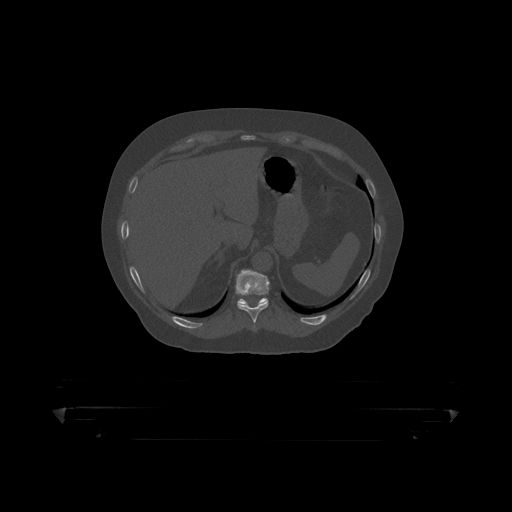
CT including the spine, one axial slice; position 210 of 390 along the scan axis; bone window (W 1800 / L 400 HU); 1.25 mm slice thickness; 512 × 512 image matrix, field of view 650 × 650 mm. Patient: male, 60 years. From the clinical record (not read from this slice): primary cancer: prostate.
Outlined on this slice (semi-automatic segmentation, software-assisted and operator-edited):
- T10 vertebra: bounding box [x1, y1, x2, y2] px = [236, 270, 270, 319]
- T11 vertebra: [238, 298, 267, 306]